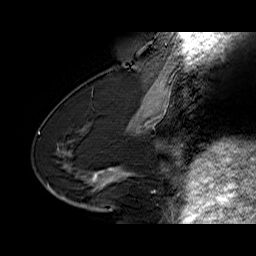
Breast MRI (dynamic contrast-enhanced), one sagittal slice. Slice 29 of 60 in the series (ordered by position). Dynamic contrast-enhanced series, time point 2 of 6 at this slice position (early post-contrast). 1.5 T. TE 6.4 ms, TR 32.9 ms. 4 mm slice thickness. 256 × 256 image matrix. Female patient. Case-level facts recorded for this patient, not image findings: setting: breast cancer imaged before/during neoadjuvant chemotherapy; receptor status: HR-positive, HER2-negative.
Structures marked on this image (semi-automatic segmentation, software-assisted and operator-edited):
- analysis volume of interest (the breast-tissue region the enhancement analysis was run in; not a lesion): bounding box [x1, y1, x2, y2] px = [68, 154, 129, 203]
- tumour enhancement mask (voxels above the 100 % enhancement threshold inside the analysis volume of interest): [91, 169, 119, 183]